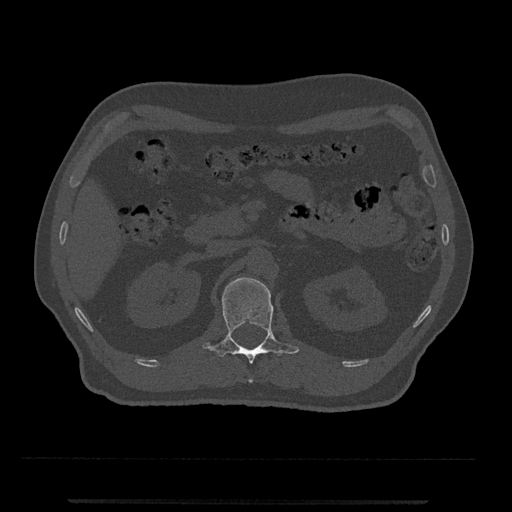
CT including the spine, one axial slice. Slice 336 of 797 in the series (ordered by position). Reconstruction kernel Br40s/3. Bone window (W 1800 / L 400 HU). 0.5 mm slice thickness. 512 × 512 image matrix, field of view 419 × 419 mm. Patient: male, 63 years. Case-level facts recorded for this patient, not image findings: primary cancer: prostate.
Annotated regions visible in this slice (semi-automatically segmented with operator editing):
- L1 vertebra: bounding box (x1, y1, x2, y2) in pixels: (202, 277, 299, 383)